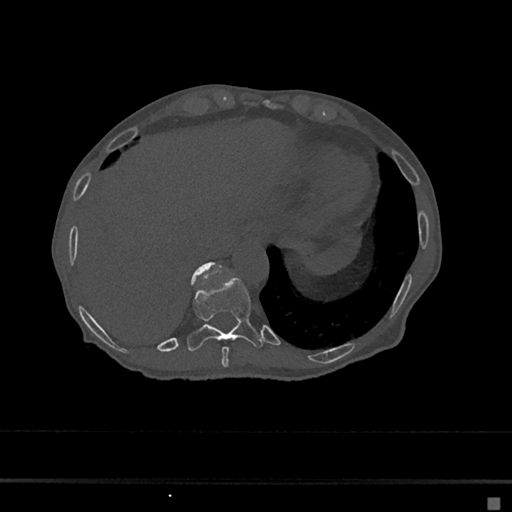
CT including the spine, one axial slice; reconstruction kernel Br40s/3; bone window (W 1800 / L 400 HU); 0.5 mm slice thickness; 512 × 512 image matrix. Patient: female, 68 years. From the clinical record (not read from this slice): primary cancer: renal.
Annotated regions visible in this slice (semi-automatic segmentation, software-assisted and operator-edited):
- T10 vertebra: bounding box [x1, y1, x2, y2] px = [187, 277, 262, 351]
- T11 vertebra: [192, 262, 222, 279]
- T9 vertebra: [221, 347, 229, 367]